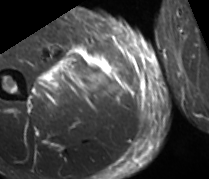
MRI of an extremity soft-tissue mass, one axial slice. Slice 27 of 89 in the series (ordered by position). STIR. MR volume resampled by the dataset authors to the PET/CT grid (not the native acquisition matrix). 3.27 mm slice thickness. 209 × 179 image matrix, field of view 204 × 175 mm. Male patient. From the clinical record (not read from this slice): histological type: undifferentiated - pleiomorphic; grade: high; site of the primary tumour: right thigh.
Structures marked on this image (expert contour drawn on MRI and transferred to this co-registered scan by the dataset authors):
- gross tumour volume including surrounding oedema: bounding box <32,48,111,102> (left, top, right, bottom; pixels)